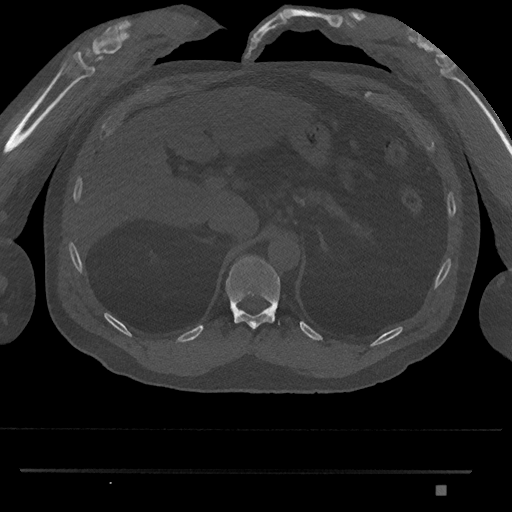
CT including the spine, one axial slice; 120 kVp; bone window (W 1800 / L 400 HU); 0.5 mm slice thickness; 512 × 512 image matrix, field of view 429 × 429 mm. Male patient, age 65 years. From the clinical record (not read from this slice): primary cancer: prostate.
Annotated regions visible in this slice (semi-automatically segmented with operator editing):
- T11 vertebra: bounding box <225,255,281,330> (left, top, right, bottom; pixels)